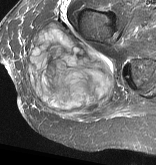
MRI of an extremity soft-tissue mass, one axial slice; position 25 of 57 along the scan axis; STIR; MR volume resampled by the dataset authors to the PET/CT grid (not the native acquisition matrix); 3.27 mm slice thickness; 156 × 165 image matrix, field of view 152 × 161 mm. Female patient. Case-level facts recorded for this patient, not image findings: histological type: epithelioid sarcoma with vascular differentiation; site of the primary tumour: right buttock.
Annotated regions visible in this slice (expert contour drawn on MRI and transferred to this co-registered scan by the dataset authors):
- gross tumour volume (mass): box from (x=26, y=23) to (x=116, y=118) px